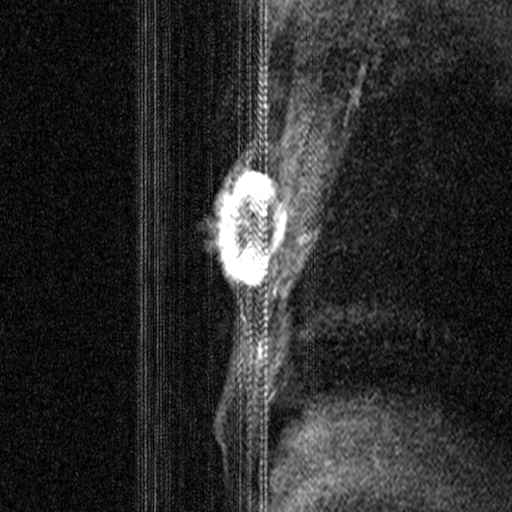
Breast MRI (dynamic contrast-enhanced), one sagittal slice; position 27 of 44 along the scan axis; dynamic contrast-enhanced study with each time point stored as its own series, time point 2 of 3 at this slice position (early post-contrast, ordered by acquisition time); 1.5 T; TE 4.5 ms, TR 11 ms; 3 mm slice thickness; 512 × 512 image matrix. Female patient, age 44 years. From the clinical record (not read from this slice): setting: breast cancer imaged before/during neoadjuvant chemotherapy; receptor status: HR-positive, HER2-negative.
Outlined on this slice (semi-automatically segmented with operator editing):
- analysis volume of interest (the breast-tissue region the enhancement analysis was run in; not a lesion): bounding box <206,164,285,299> (left, top, right, bottom; pixels)
- tumour enhancement mask (voxels above the 90 % enhancement threshold inside the analysis volume of interest): <218,164,285,295>